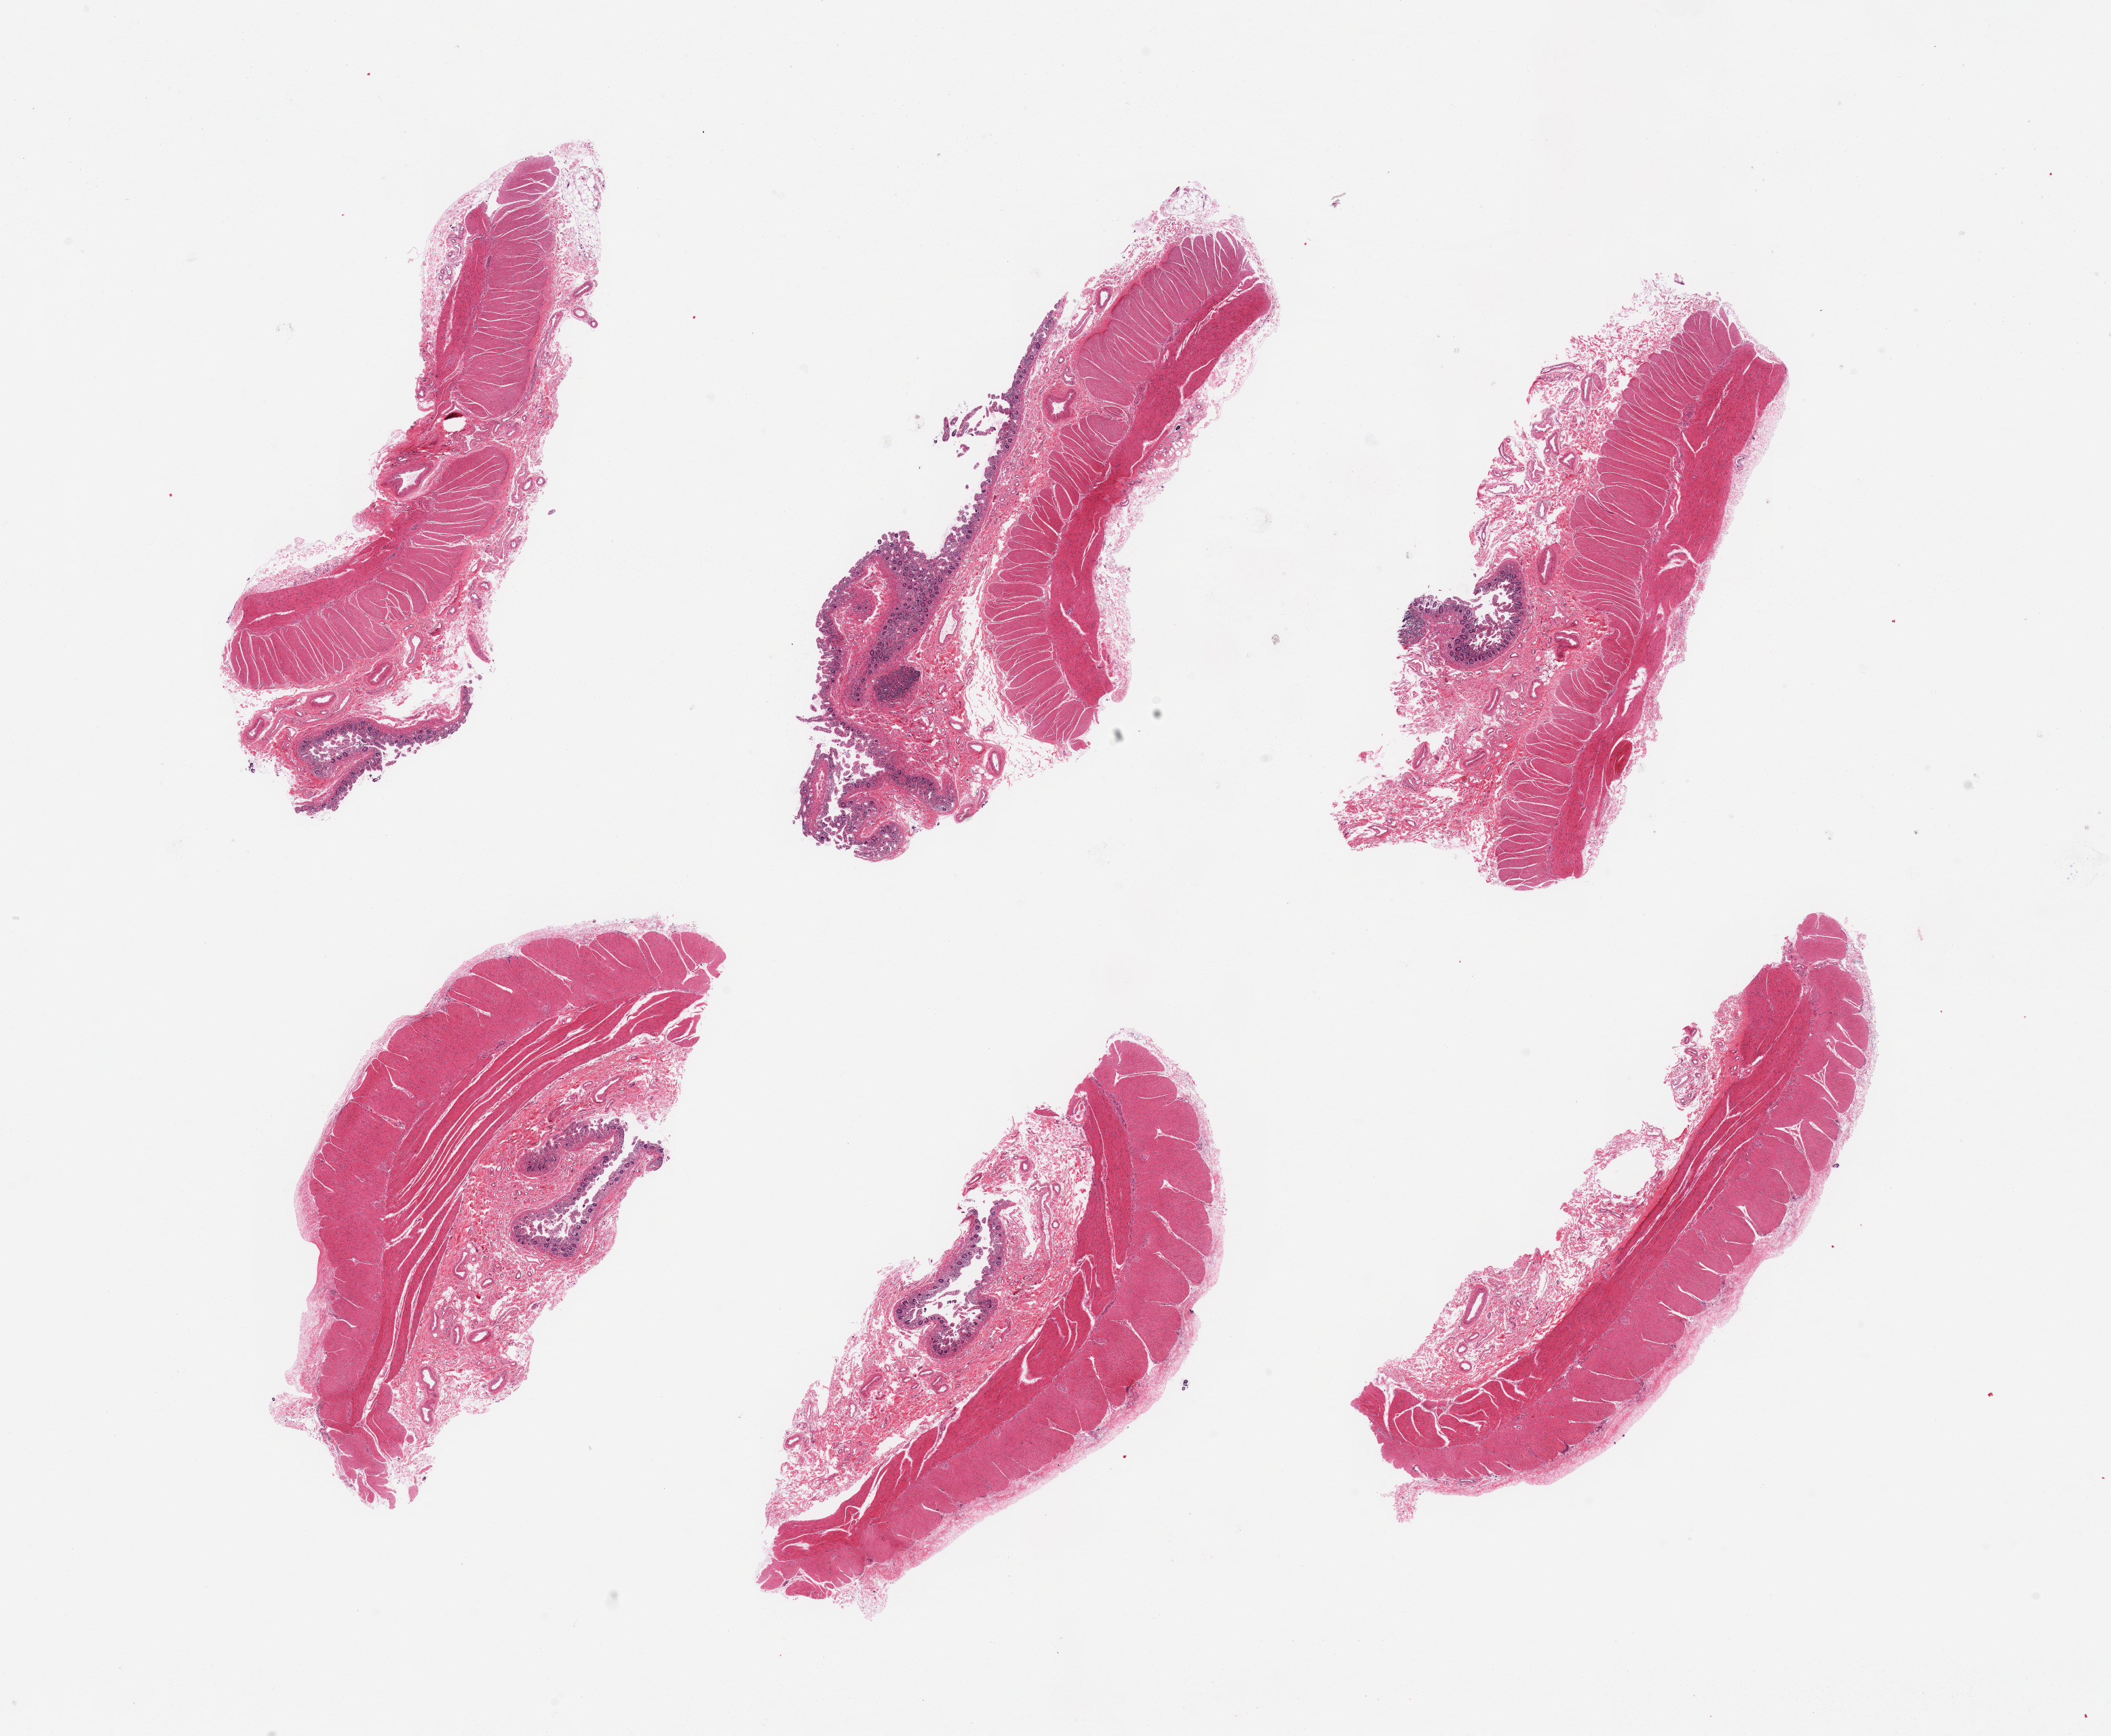
Digitized H&E-stained section, whole scanned area (about 24.6 x 20.2 mm) shown as a low-resolution overview; PAXgene-fixed, paraffin-embedded tissue; section of ileum (target tissue); donor tissue sample. Male donor.
Pathologist's review note for this sample: 6 pieces anatomic correct organ, only trace target lymphoid aggregates.